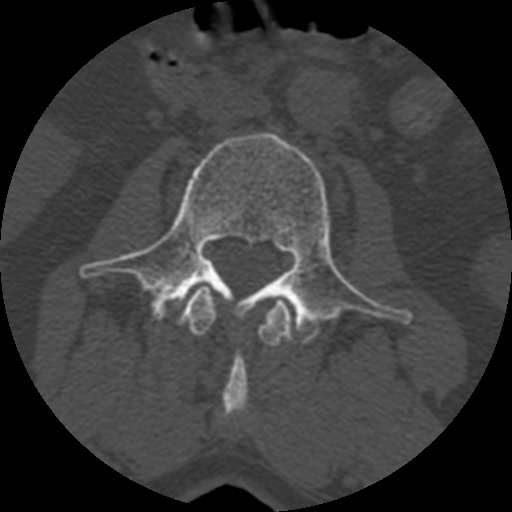
CT including the spine, one axial slice; reconstruction kernel STANDARD; bone window (W 1800 / L 400 HU); 1.25 mm slice thickness; 512 × 512 image matrix. Patient age 71 years. From the clinical record (not read from this slice): primary cancer: prostate.
Structures marked on this image (semi-automatically segmented with operator editing):
- L2 vertebra: bounding box [x1, y1, x2, y2] px = [178, 287, 292, 419]
- L3 vertebra: [79, 132, 406, 343]